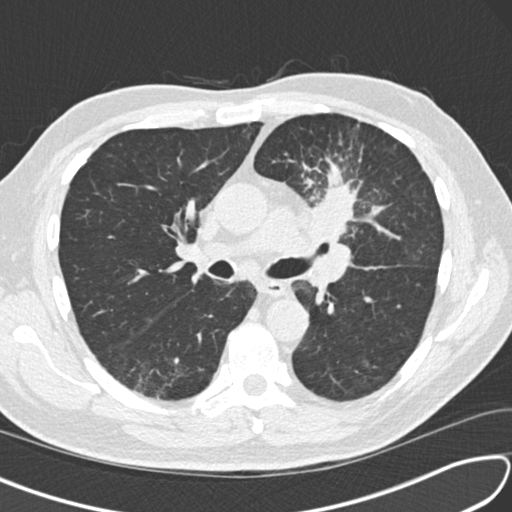
Low-dose screening chest CT, one axial slice. Slice 93 of 156 in the series (ordered by position). 120 kVp. Lung window (W 1500 / L -600 HU). 512 × 512 image matrix, field of view 340 × 340 mm.
Outlined on this slice (expert manual segmentation):
- lesion 1 (tumor, upper lobe of left lung): bounding box <308,183,356,242> (left, top, right, bottom; pixels)